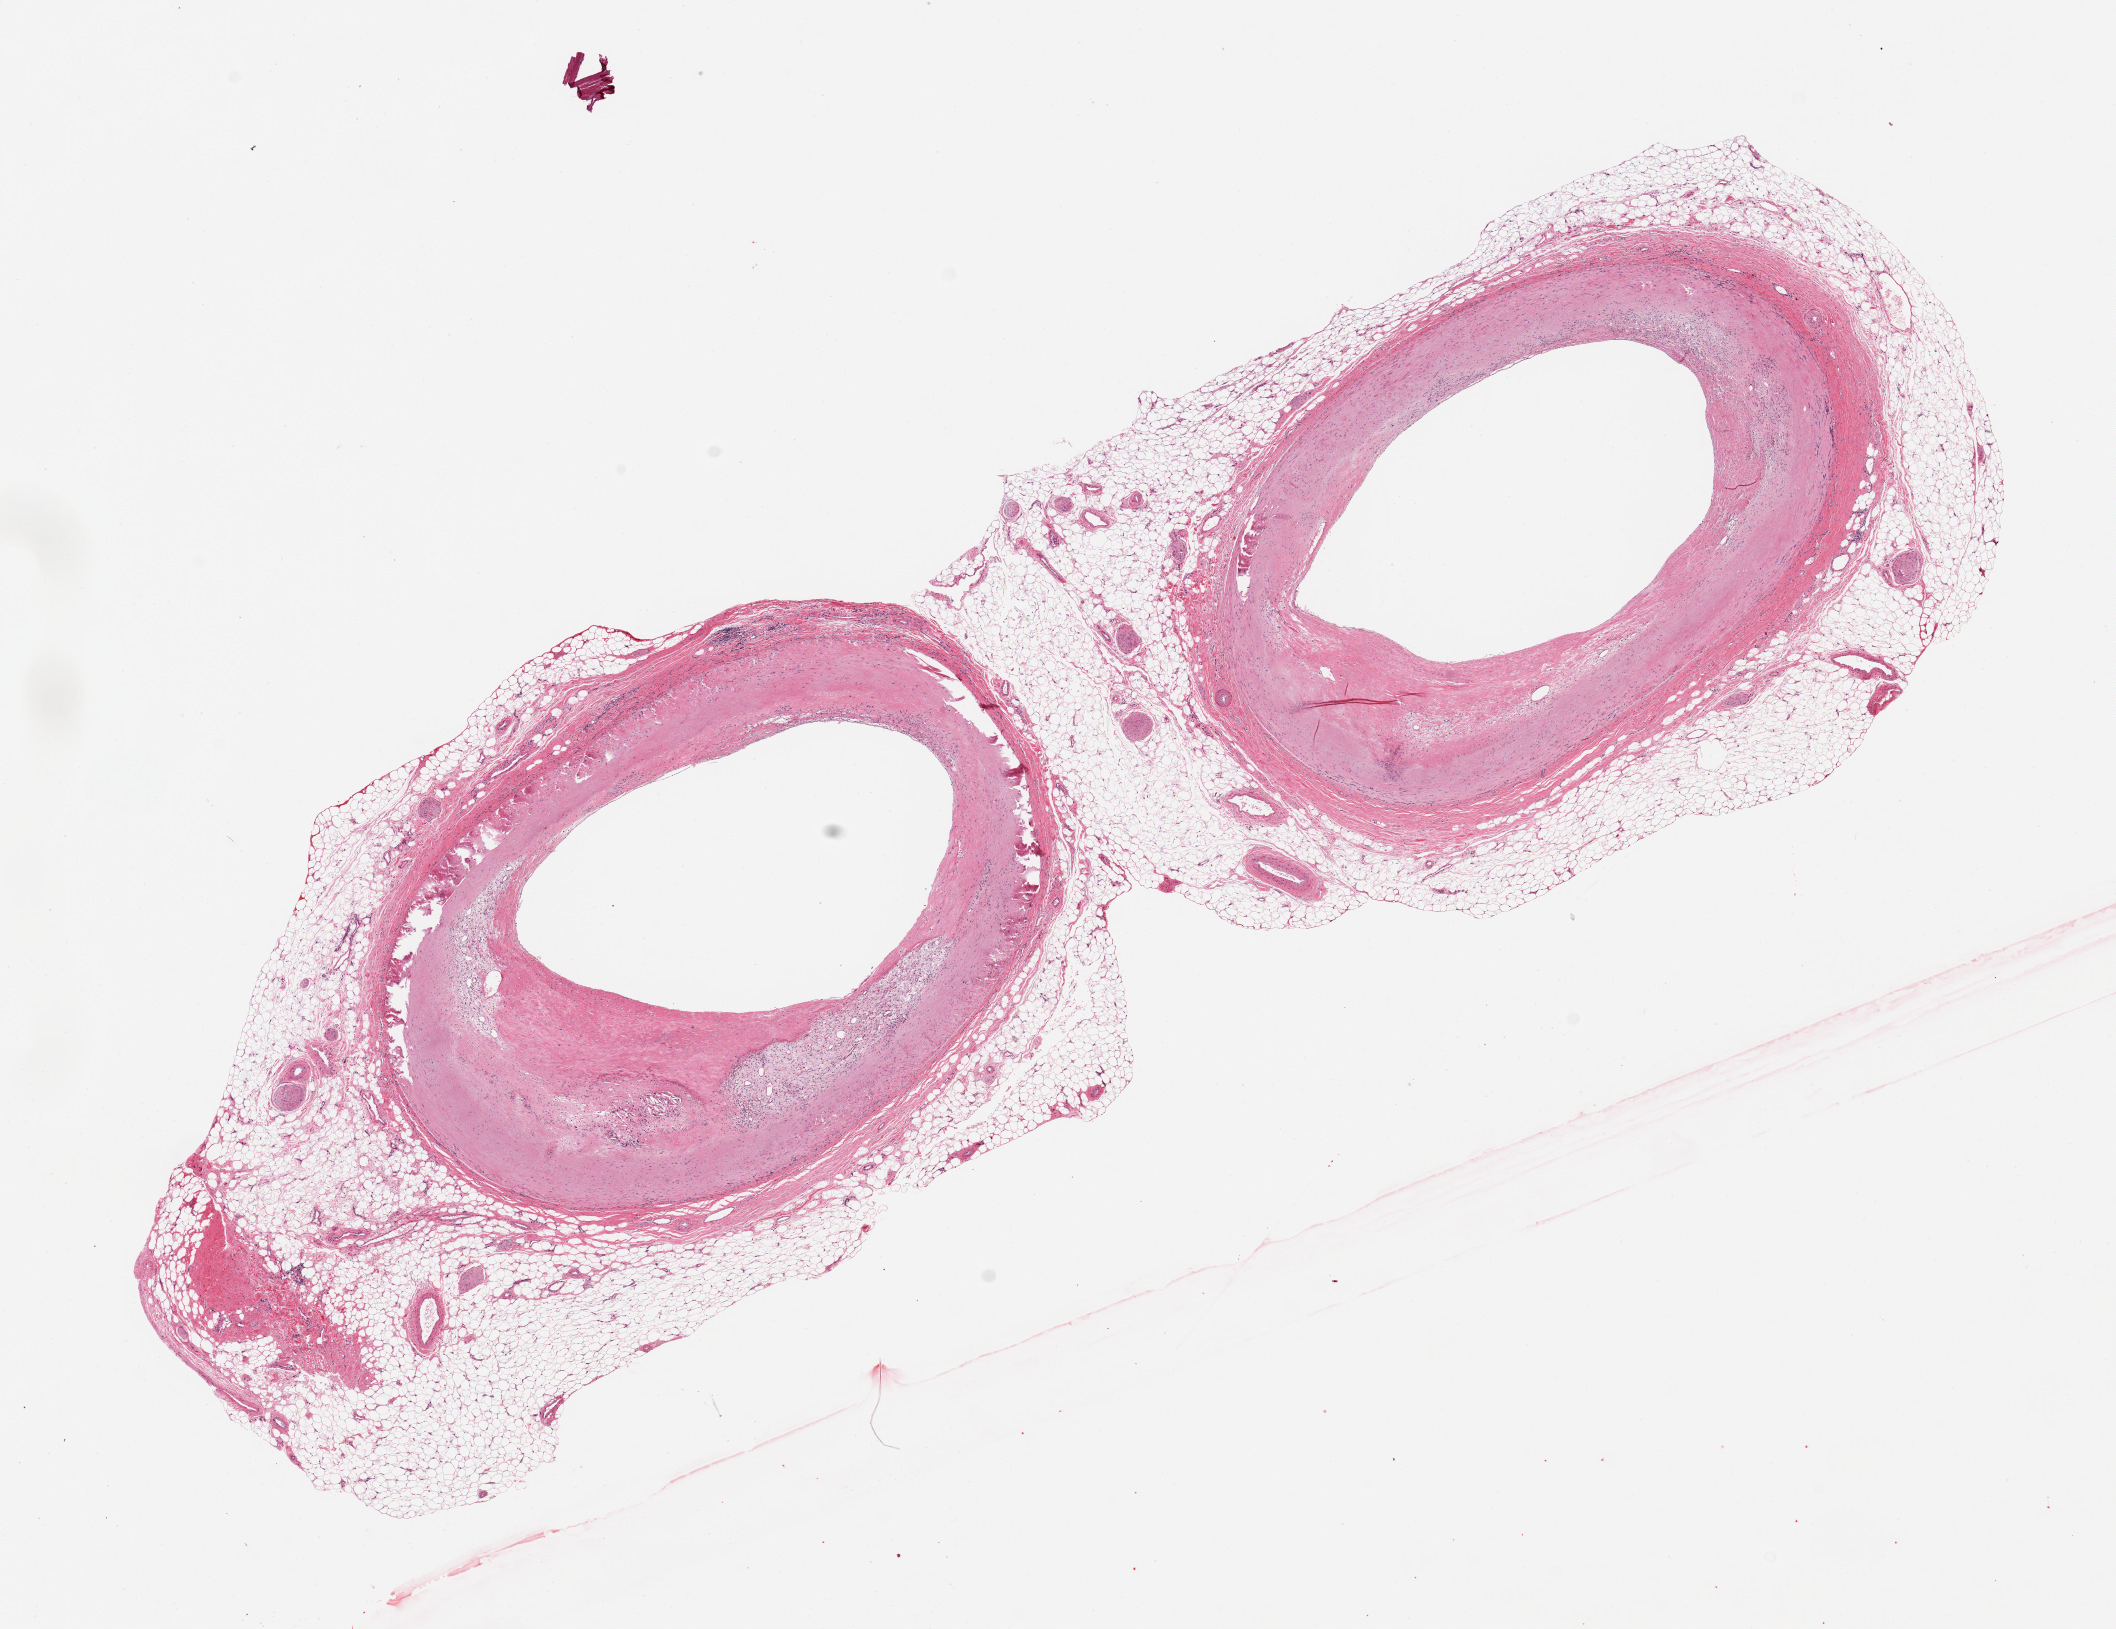
Whole-slide image, H&E stain, low-resolution overview of the scanned area, about 16.7 x 12.9 mm (acquisition: 20x scan); PAXgene-fixed, paraffin-embedded tissue; section of coronary artery (target tissue); donor tissue sample.
Pathologist's review note for this sample: 2 pieces 8x5 & 7x5 mm; eccentric plaques with wide lumens; 40% external adipose.